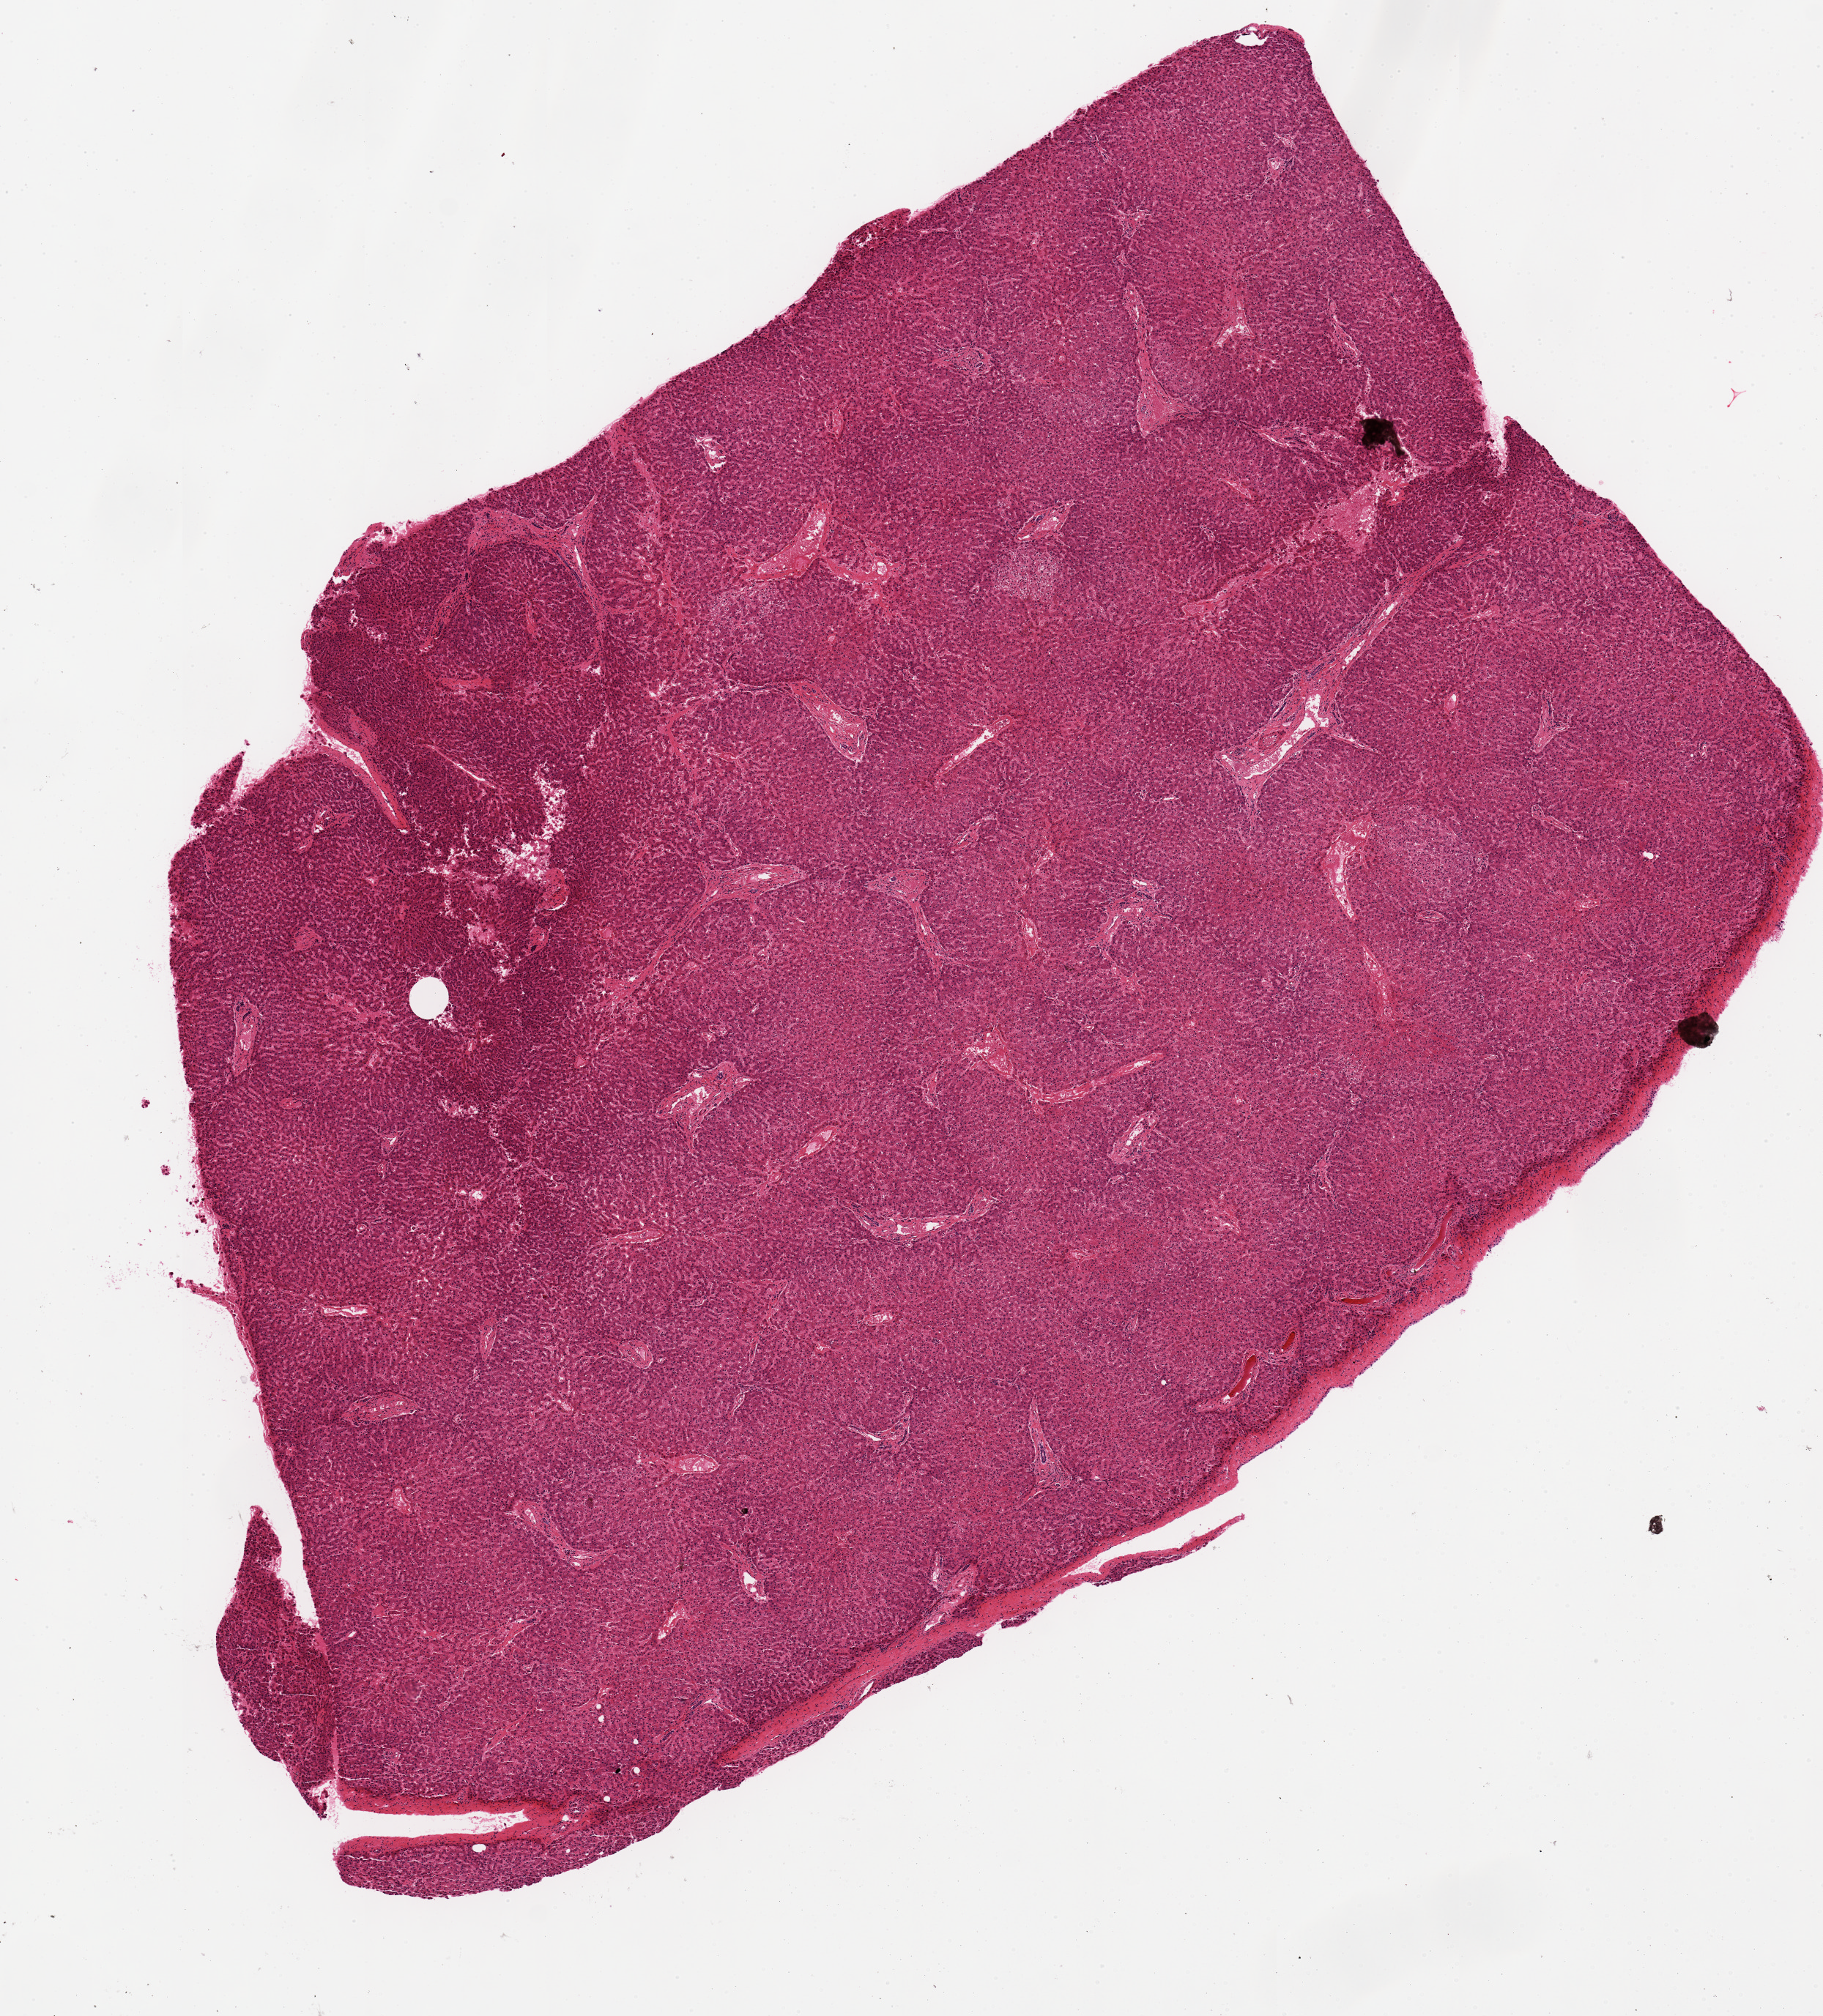
Digitized haematoxylin and eosin-stained section, brightfield, whole scanned area (about 9.8 x 10.9 mm) shown as a low-resolution overview; PAXgene-fixed, paraffin-embedded tissue; sampled site (target tissue): liver; tissue donor sample. Donor: male.
Pathologist's review note for this sample: 11 x 6.8mm. Focal area poor fixation, hole/tears.